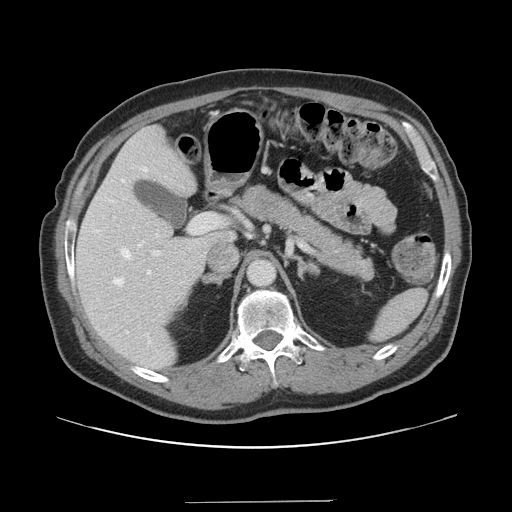
Contrast-enhanced abdominal CT, one axial slice; position 90 of 151 along the scan axis; 120 kVp; intravenous contrast given; soft-tissue window (W 400 / L 40 HU); 2.5 mm slice thickness; 512 × 512 image matrix, field of view 399 × 399 mm. Male patient, age 63 years. Case-level facts recorded for this patient, not image findings: diagnosis: colorectal cancer liver metastases, imaged before liver resection; multiple liver metastases: no; largest metastasis: 2.1 cm.
Outlined on this slice (outlined manually by an expert reader):
- hepatic veins: bounding box <113,167,152,344> (left, top, right, bottom; pixels)
- liver: <77,127,233,370>
- planned liver remnant (the part of the liver to remain after resection): <76,127,232,370>
- portal vein (with intrahepatic branches): <152,213,221,257>